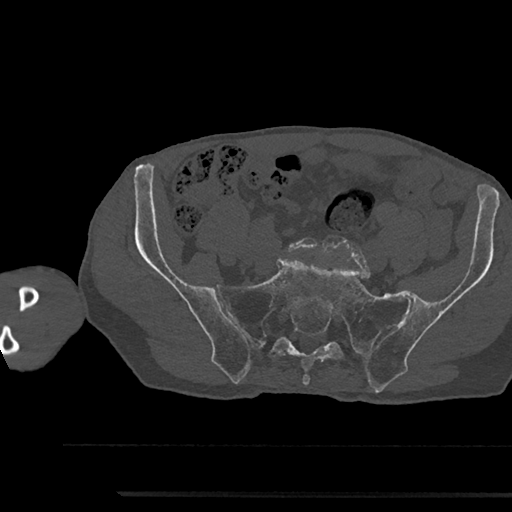
CT including the spine, one axial slice; position 280 of 797 along the scan axis; reconstruction kernel Br40s/3; 120 kVp; bone window (W 1800 / L 400 HU); 0.5 mm slice thickness; 512 × 512 image matrix, field of view 367 × 367 mm. Male patient, age 79 years. From the clinical record (not read from this slice): primary cancer: prostate.
Structures marked on this image (semi-automatically segmented with operator editing):
- L5 vertebra: bounding box (x1, y1, x2, y2) in pixels: (288, 237, 318, 251)